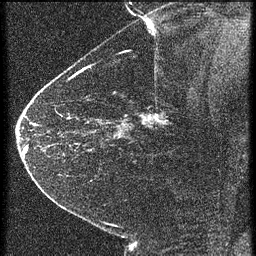
Breast MRI (dynamic contrast-enhanced), one sagittal slice. 4 images stored at this slice position (order not interpretable as contrast timing). 1.5 T. TE 4.2 ms, TR 21.3 ms. 1.5 mm slice thickness. 256 × 256 image matrix, field of view 180 × 180 mm. Patient: female, 43 years. Case-level facts recorded for this patient, not image findings: setting: breast cancer imaged before/during neoadjuvant chemotherapy; receptor status: HER2-positive.
Annotated regions visible in this slice (semi-automatic segmentation, software-assisted and operator-edited):
- analysis volume of interest (the breast-tissue region the enhancement analysis was run in; not a lesion): bounding box <122,100,187,151> (left, top, right, bottom; pixels)
- tumour enhancement mask (voxels above the 90 % enhancement threshold inside the analysis volume of interest): <144,114,165,125>